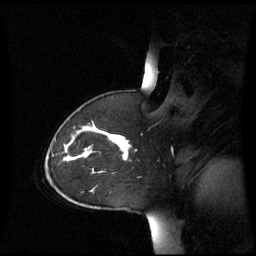
Breast MRI (dynamic contrast-enhanced), one sagittal slice; position 44 of 60 along the scan axis; dynamic contrast-enhanced series, image 2 of 3 at this slice position (ordered by acquisition); 1.5 T; TE 4.2 ms, TR 8.4 ms; 256 × 256 image matrix, field of view 270 × 270 mm. Patient: female, 43 years. Case-level facts recorded for this patient, not image findings: setting: breast cancer imaged before/during neoadjuvant chemotherapy; receptor status: triple-negative.
Outlined on this slice (semi-automatic segmentation, software-assisted and operator-edited):
- analysis volume of interest (the breast-tissue region the enhancement analysis was run in; not a lesion): bounding box (x1, y1, x2, y2) in pixels: (55, 124, 130, 173)
- tumour enhancement mask (voxels above the 70 % enhancement threshold inside the analysis volume of interest): (70, 134, 130, 160)